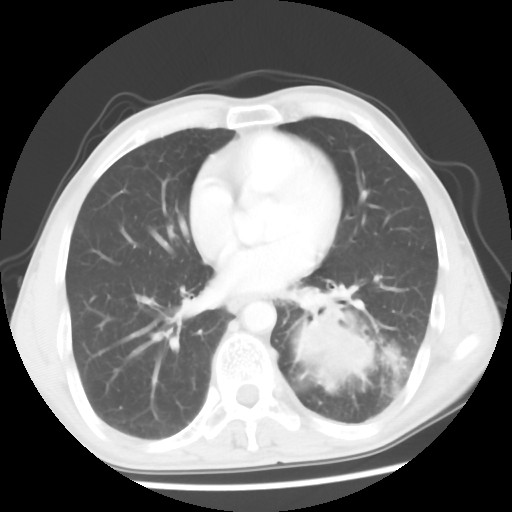
Chest CT, one axial slice; position 25 of 56 along the scan axis; 120 kVp; lung window (W 1500 / L -600 HU); 5 mm slice thickness; 512 × 512 image matrix. Male patient, age 60 years. From the clinical record (not read from this slice): clinical TNM (as recorded): T4 N0 M0.
Annotated regions visible in this slice (bounding box drawn by a radiologist):
- lung tumour (recorded histology: squamous cell carcinoma): bounding box (x1, y1, x2, y2) in pixels: (281, 306, 393, 396)